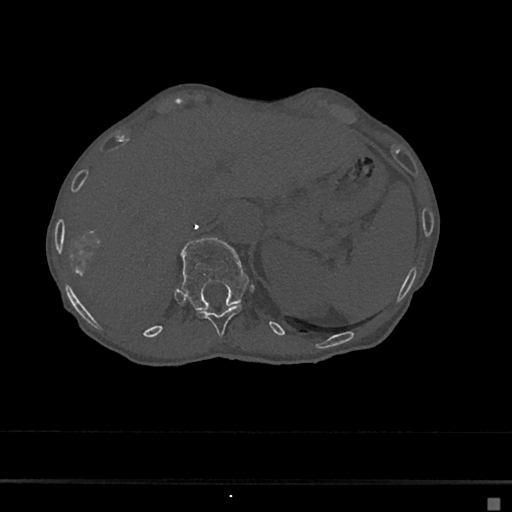
CT including the spine, one axial slice; slice 143 of 797 in the series (ordered by position); reconstruction kernel Br40s/3; 120 kVp; bone window (W 1800 / L 400 HU); 0.5 mm slice thickness; 512 × 512 image matrix, field of view 360 × 360 mm. Patient: female, 68 years. Case-level facts recorded for this patient, not image findings: primary cancer: renal.
Structures marked on this image (semi-automatic segmentation, software-assisted and operator-edited):
- T11 vertebra: bounding box <196,304,243,336> (left, top, right, bottom; pixels)
- T12 vertebra: <181,238,249,311>